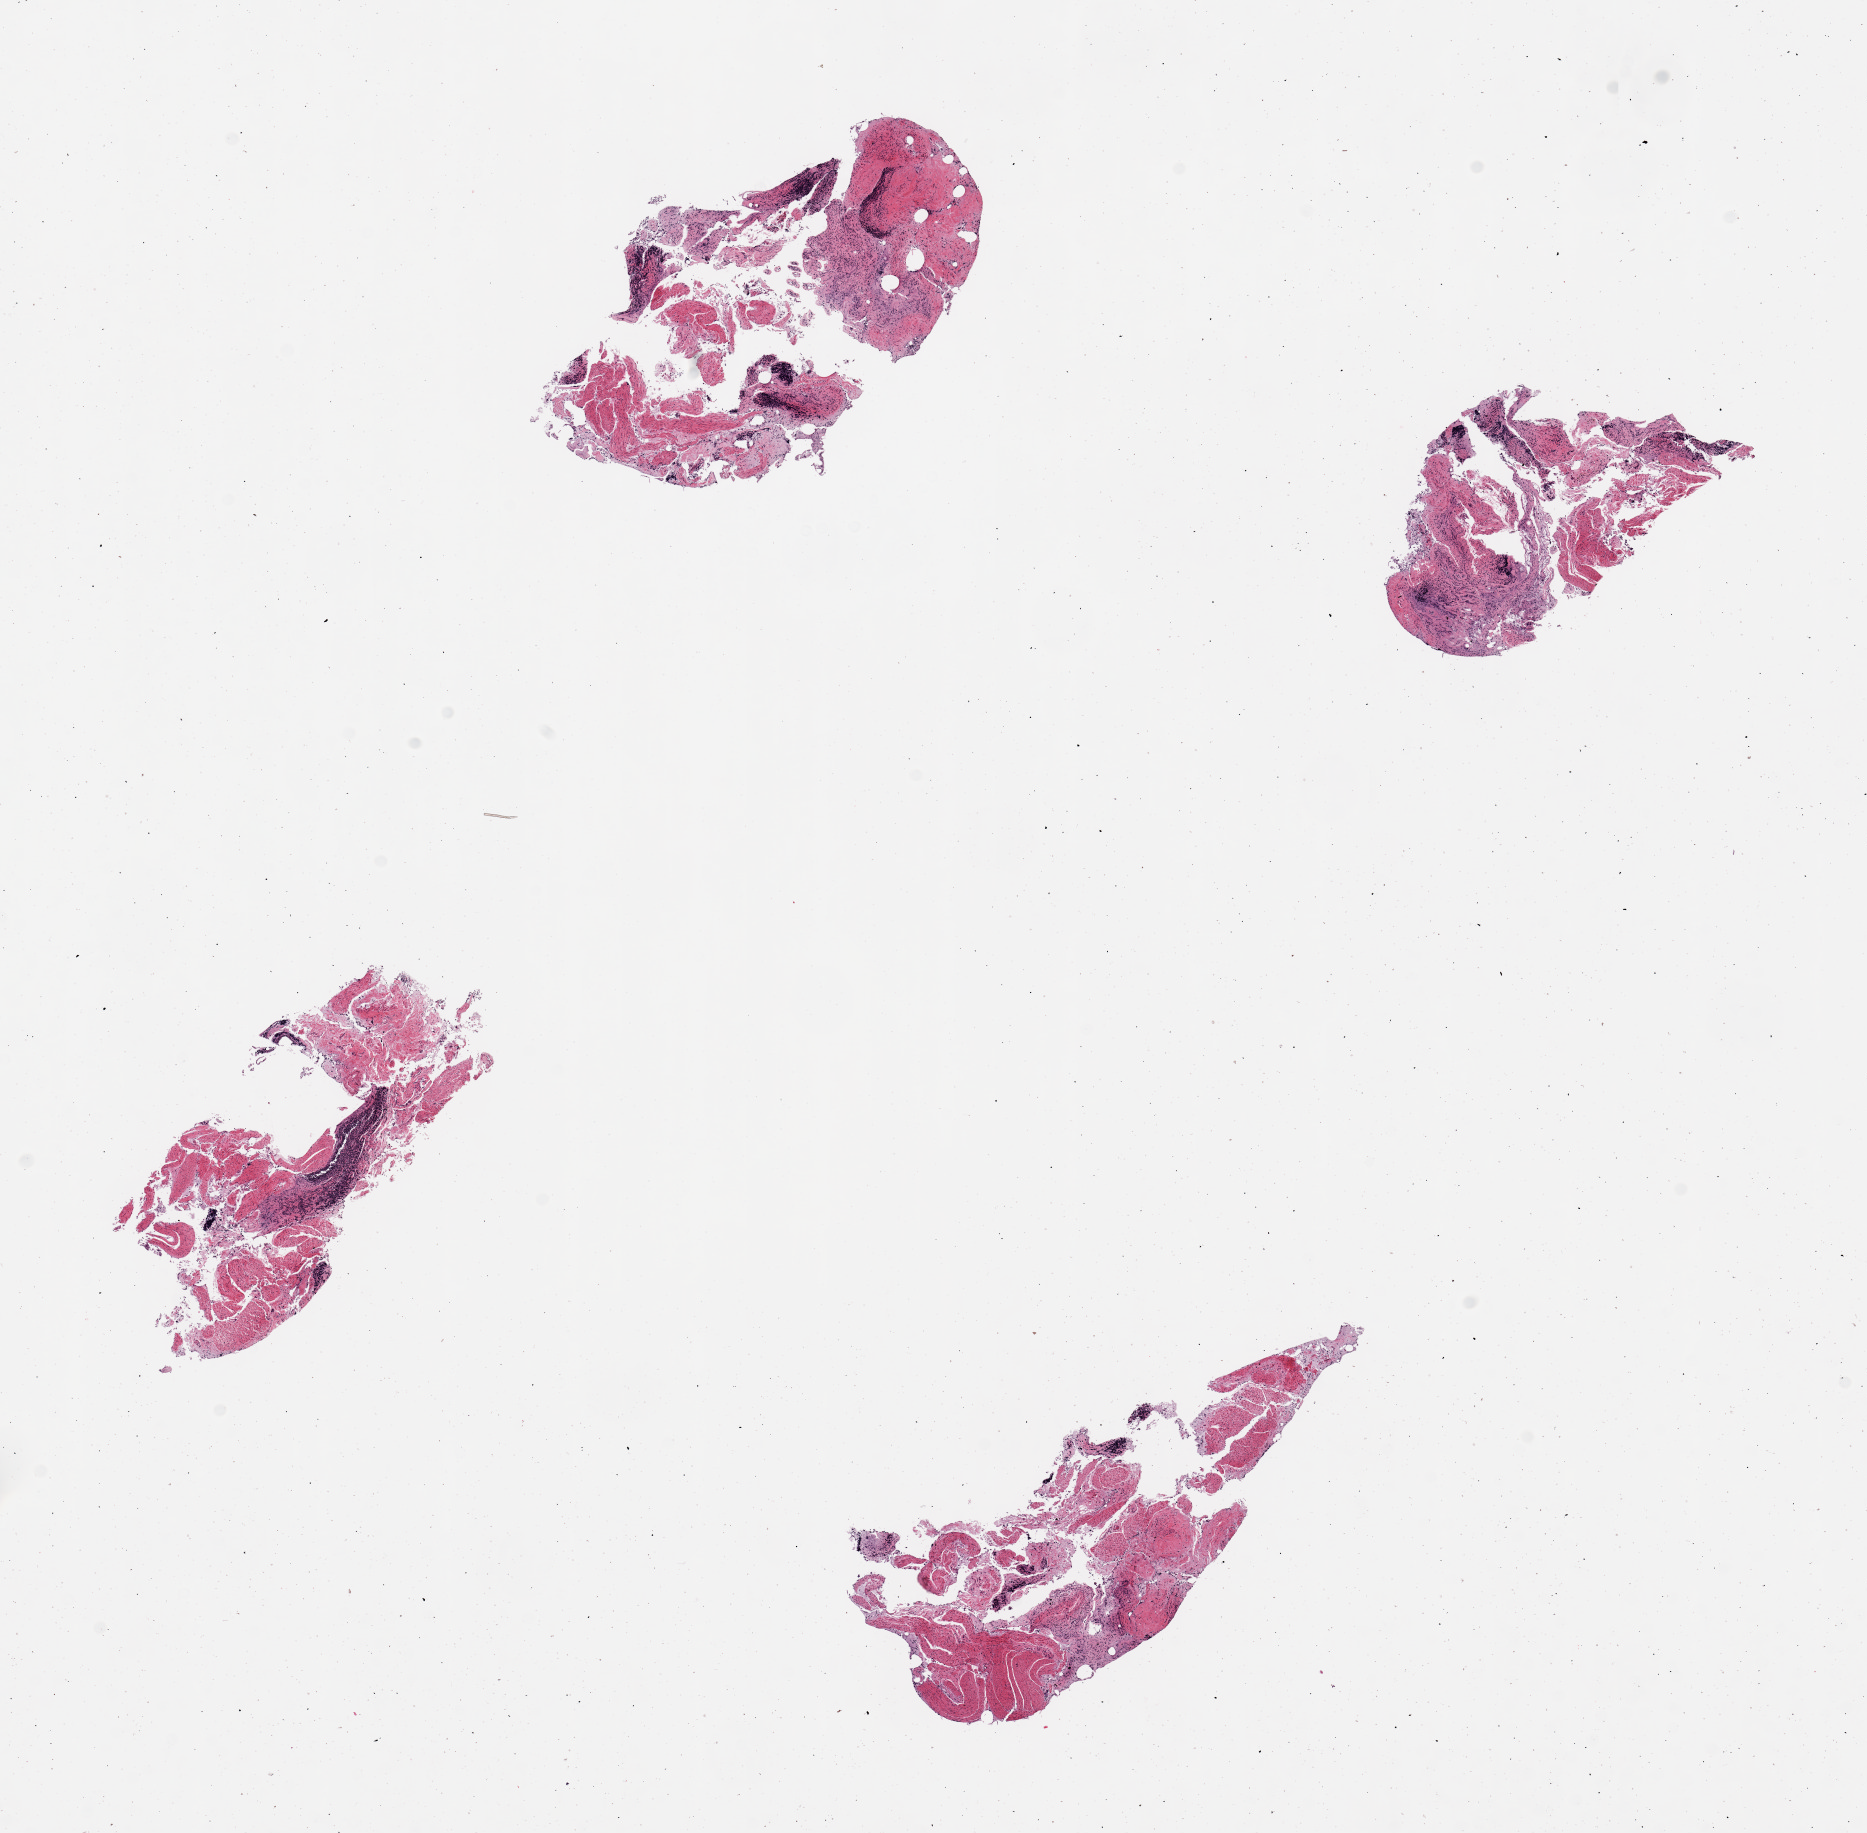
Haematoxylin and eosin whole-slide image, brightfield — shown as a low-resolution overview of the whole scanned area (about 14.8 x 14.5 mm), PAXgene-fixed paraffin-embedded (PFPE) section, section of ileum (target tissue), donor tissue sample. Donor: female.
Pathologist's review note for this sample: 4 pieces; insufficient lymphoid tissue.